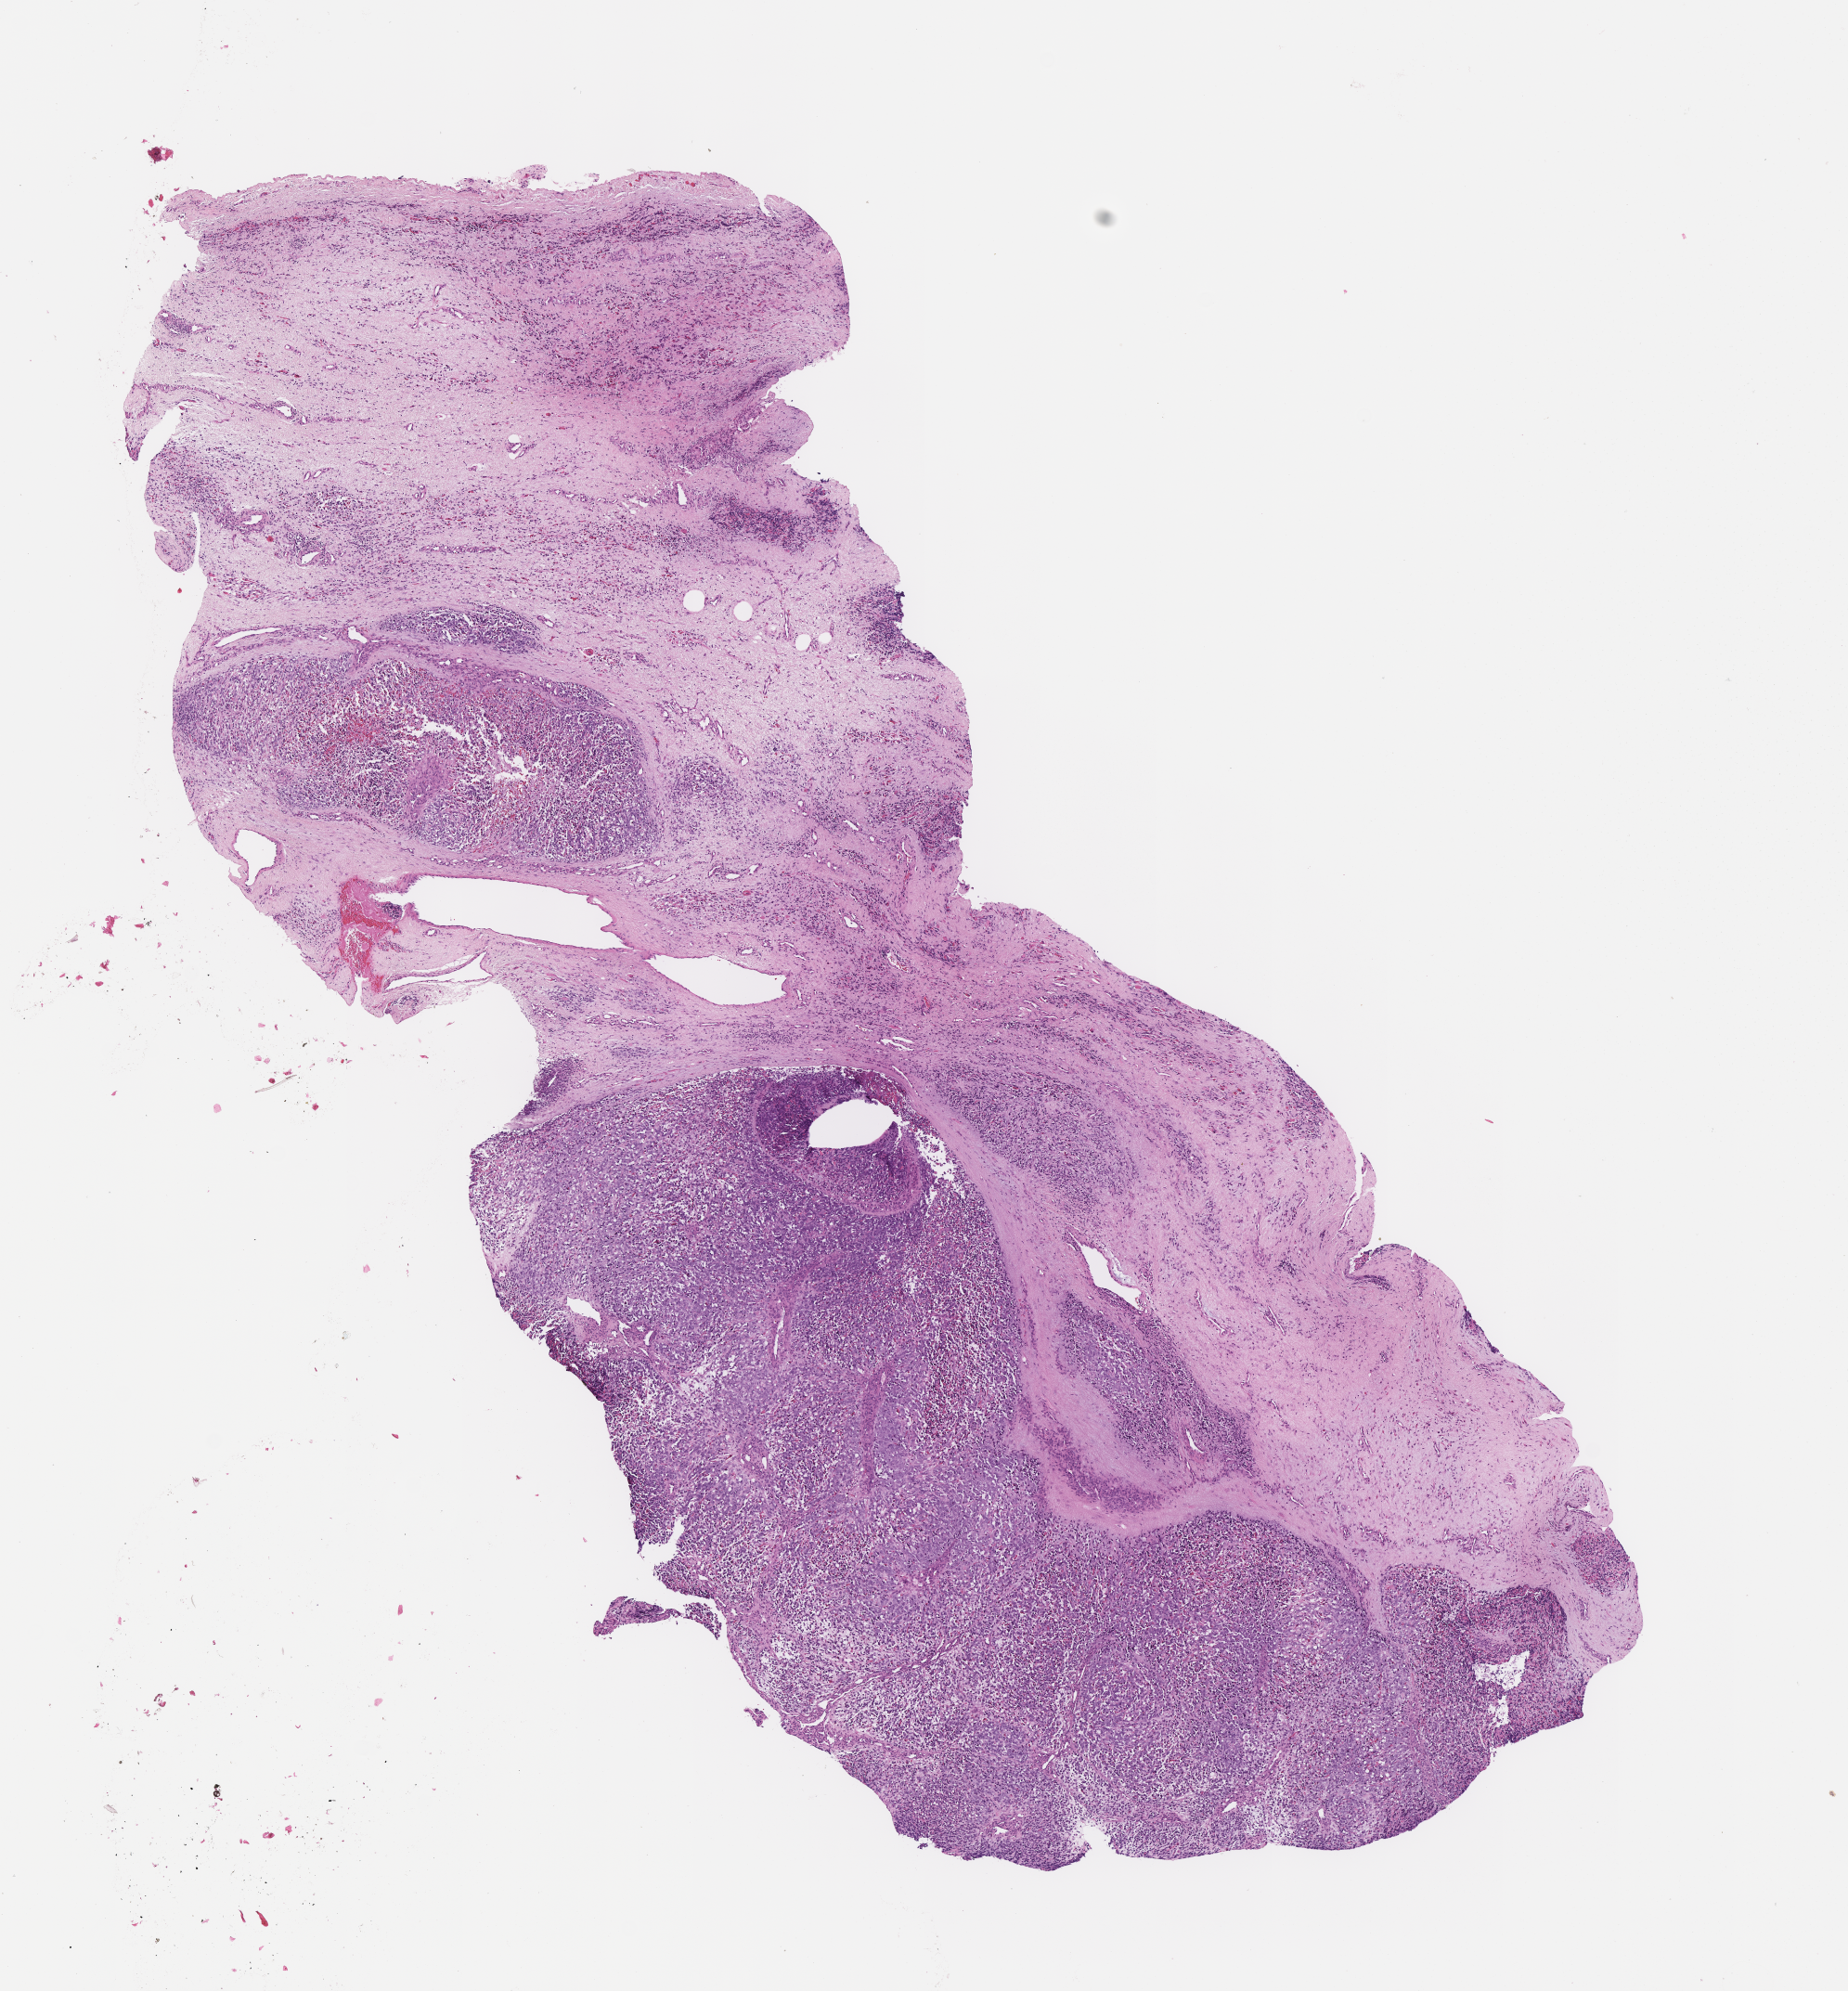
Whole-slide image, H&E stain of tumor tissue — whole scanned area (about 8.1 x 8.7 mm) shown as a low-resolution overview. Formalin-fixed paraffin-embedded section. Site: testicle, right. Patient: male, age 5.5 years at diagnosis.
Stage (as recorded): 1. Metastatic status at presentation (as recorded): non-metastatic (confirmed). Diagnosis: rhabdomyosarcoma; histological classification: embryonal rhabdomyosarcoma.